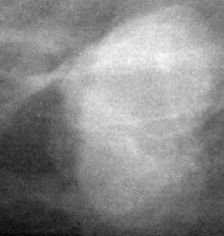
Crop from a digitized film mammogram around one marked abnormality; right breast; MLO view; BI-RADS breast density category 1 (scale 1–4).
- Mass, shape lobulated, margins circumscribed / ill defined; BI-RADS assessment category 4; pathology result (as recorded, not read from the image): malignant.